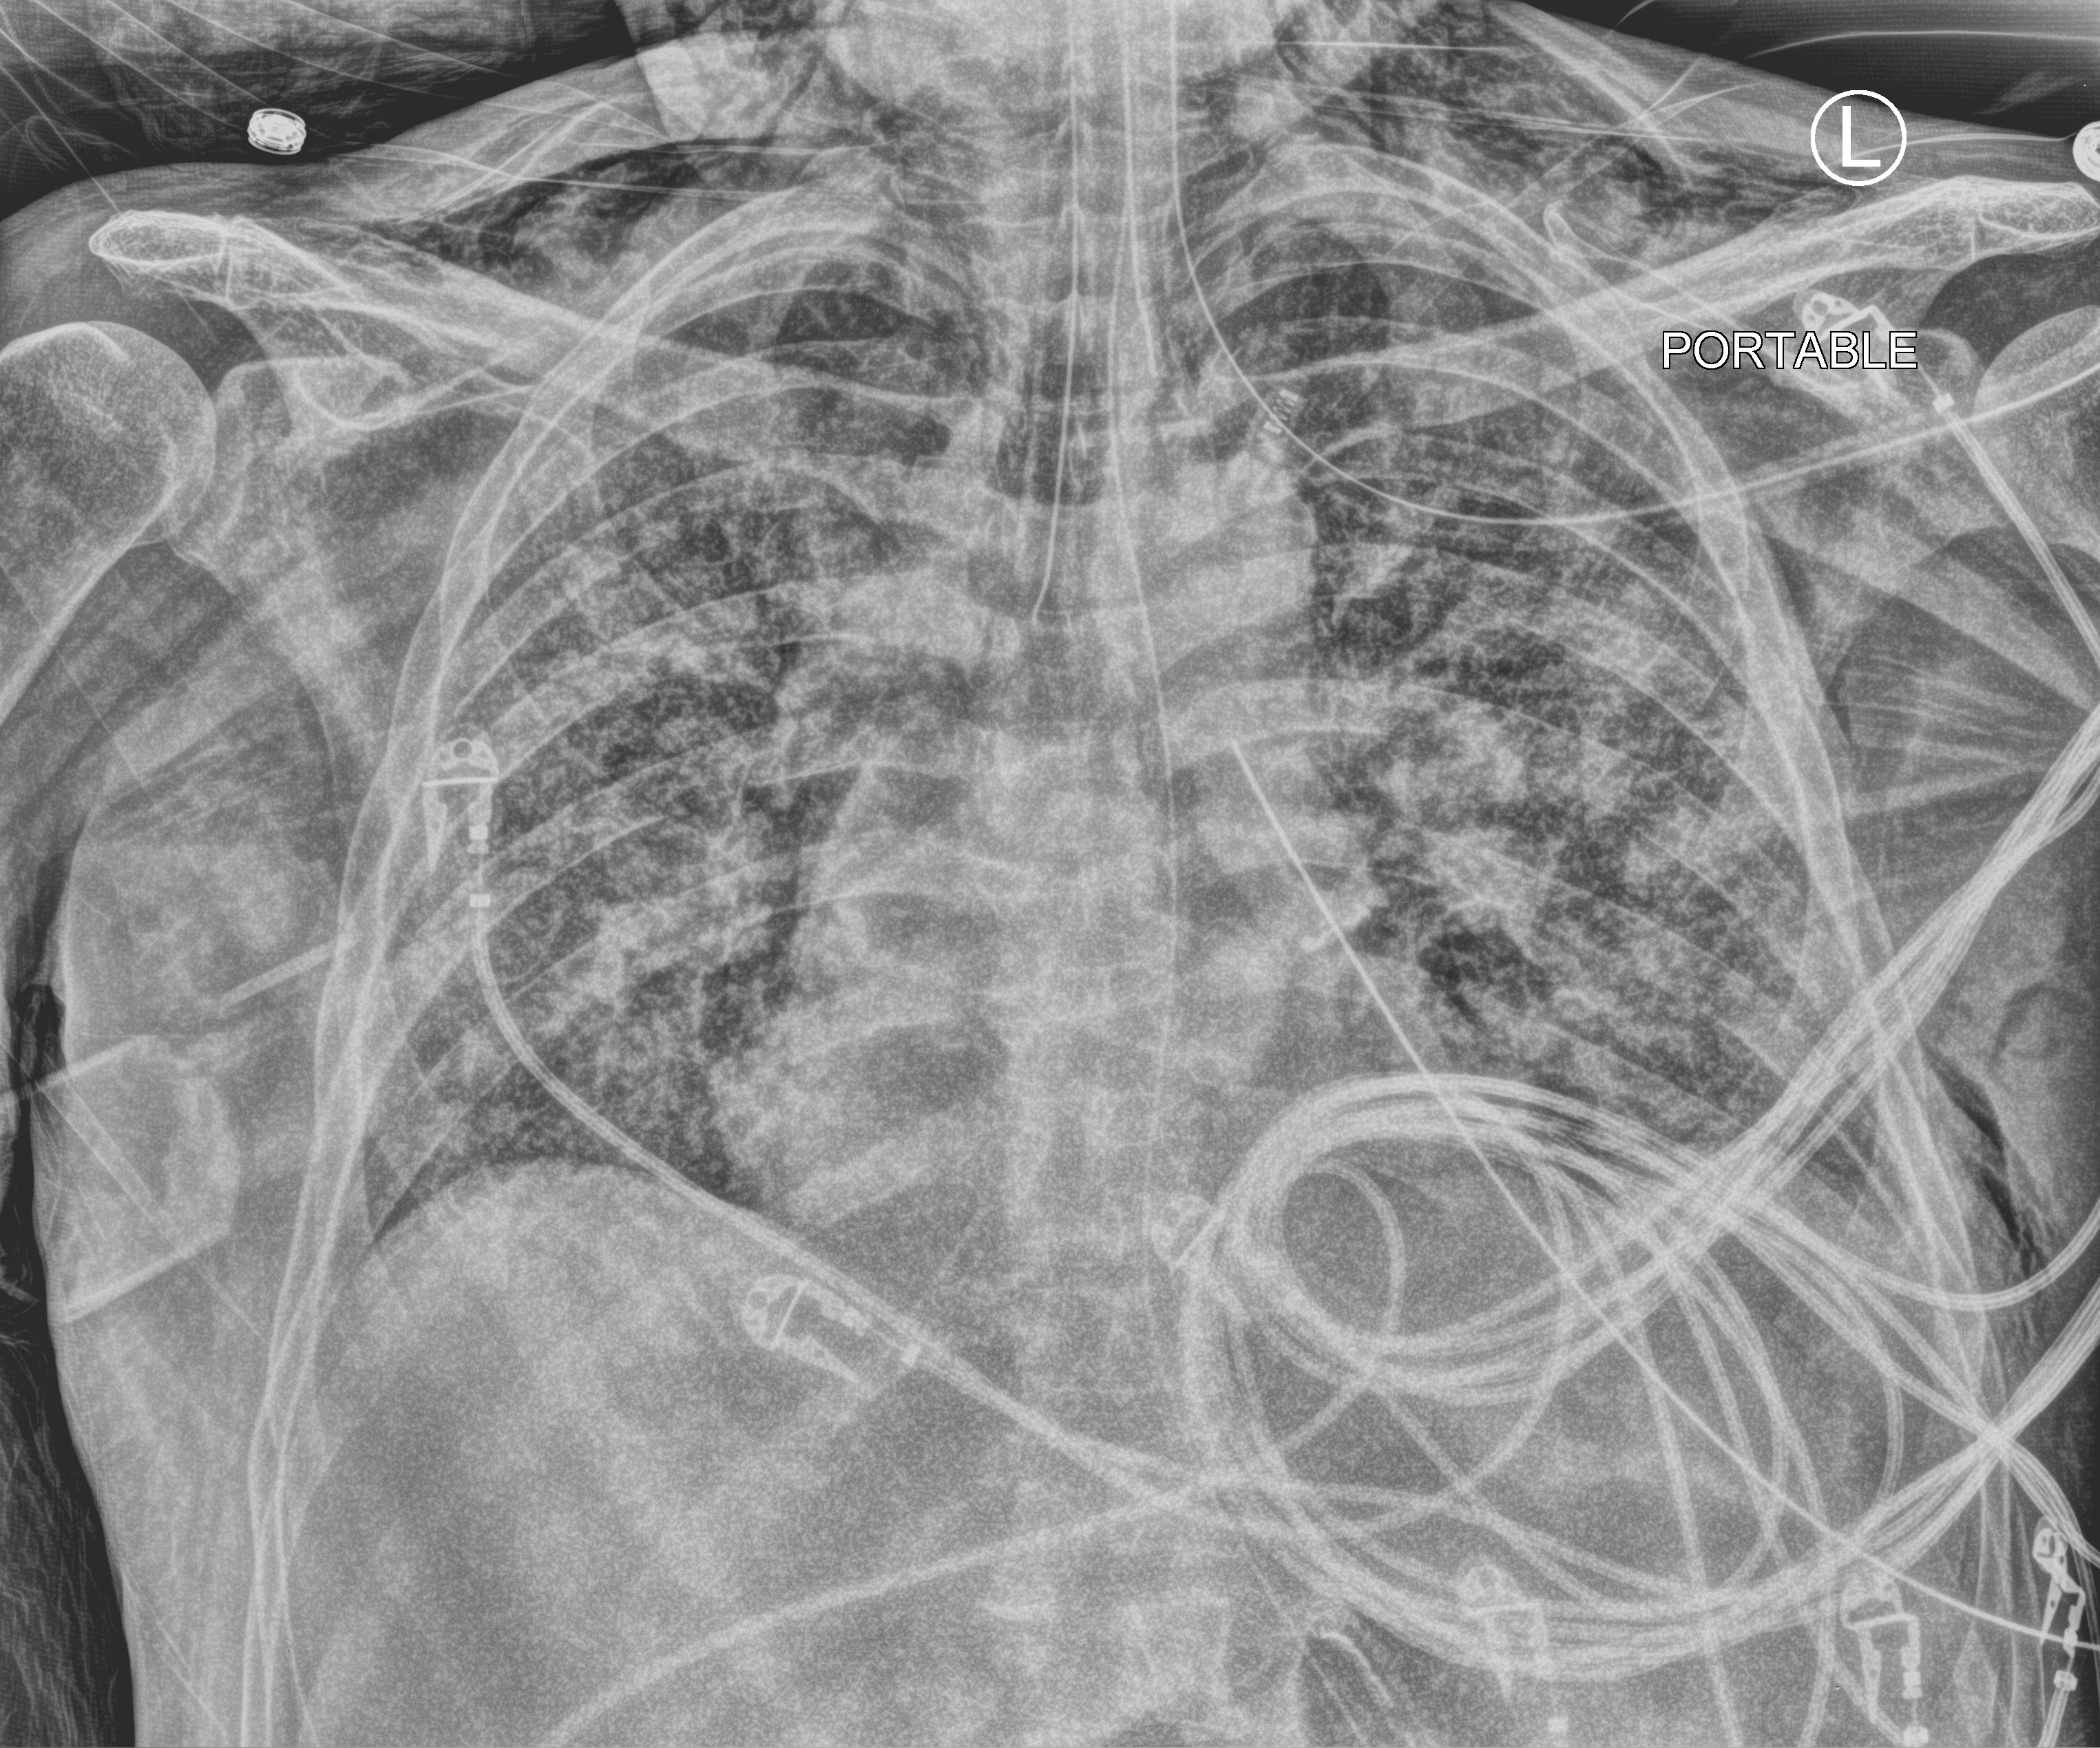
Bedside chest radiograph (computed radiography). Patient hospitalised with COVID-19; male, aged 60–74 years.
Admission-level facts for this patient (not findings on this image; timing relative to this image not recorded):
- admitted to intensive care during this hospital stay: yes
- mechanically ventilated during this hospital stay: yes